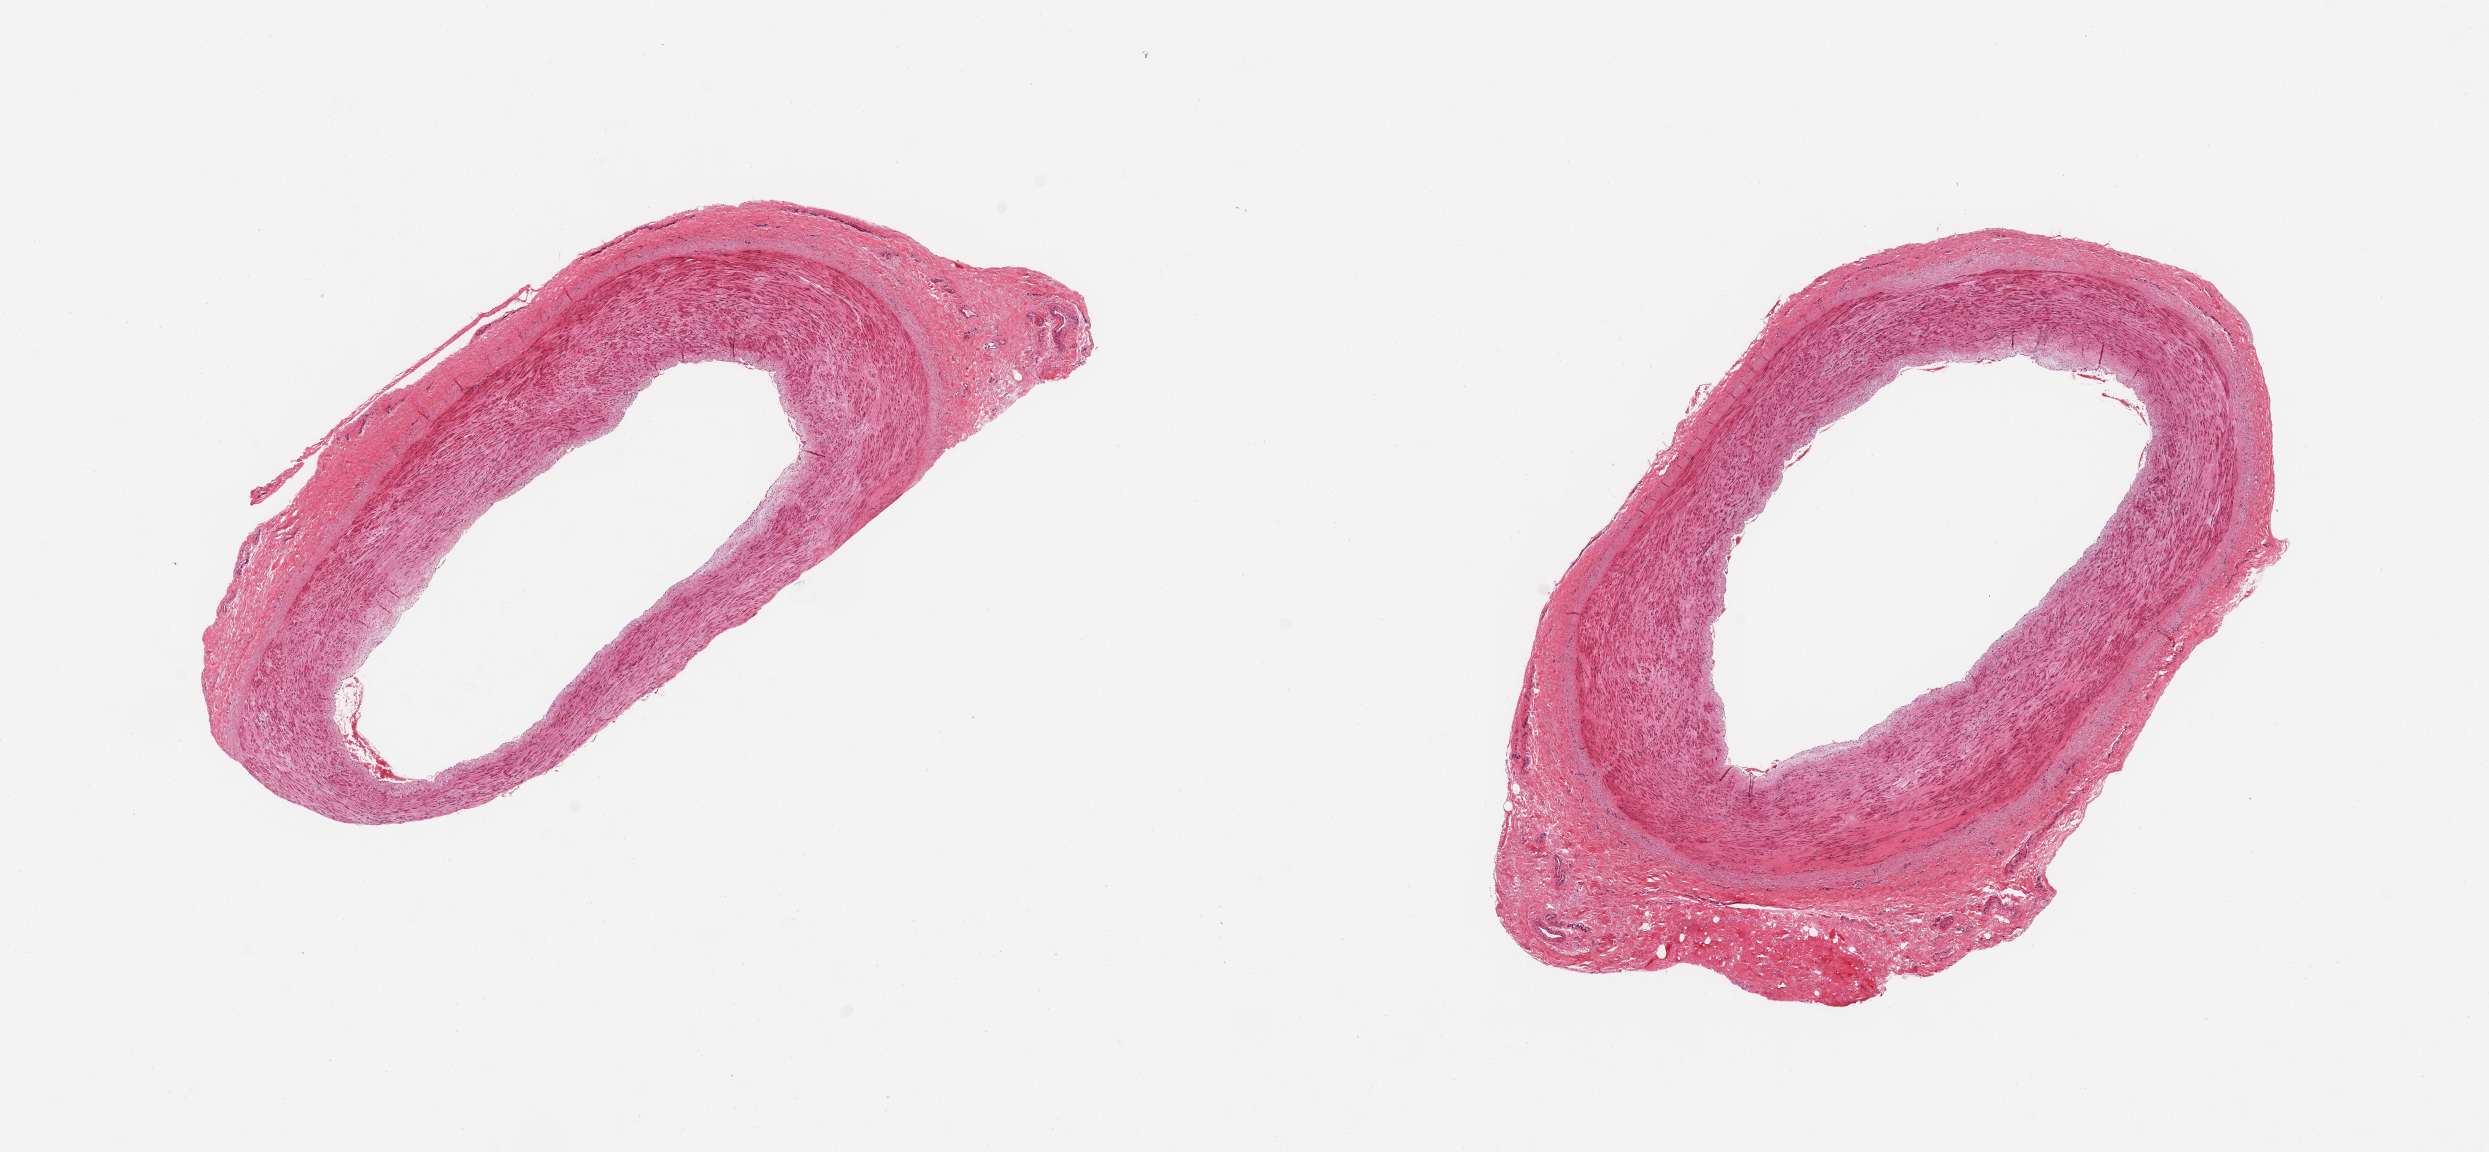
Whole-slide image, H&E stain — whole scanned area (about 19.7 x 9.1 mm) shown as a low-resolution overview. PAXgene-fixed, paraffin-embedded tissue. Target tissue: tibial artery. Tissue donor sample. Male donor.
Pathologist's review note for this sample: 2 pieces, variable peripheral rim adherent fibrous tissue up to ~1mm.